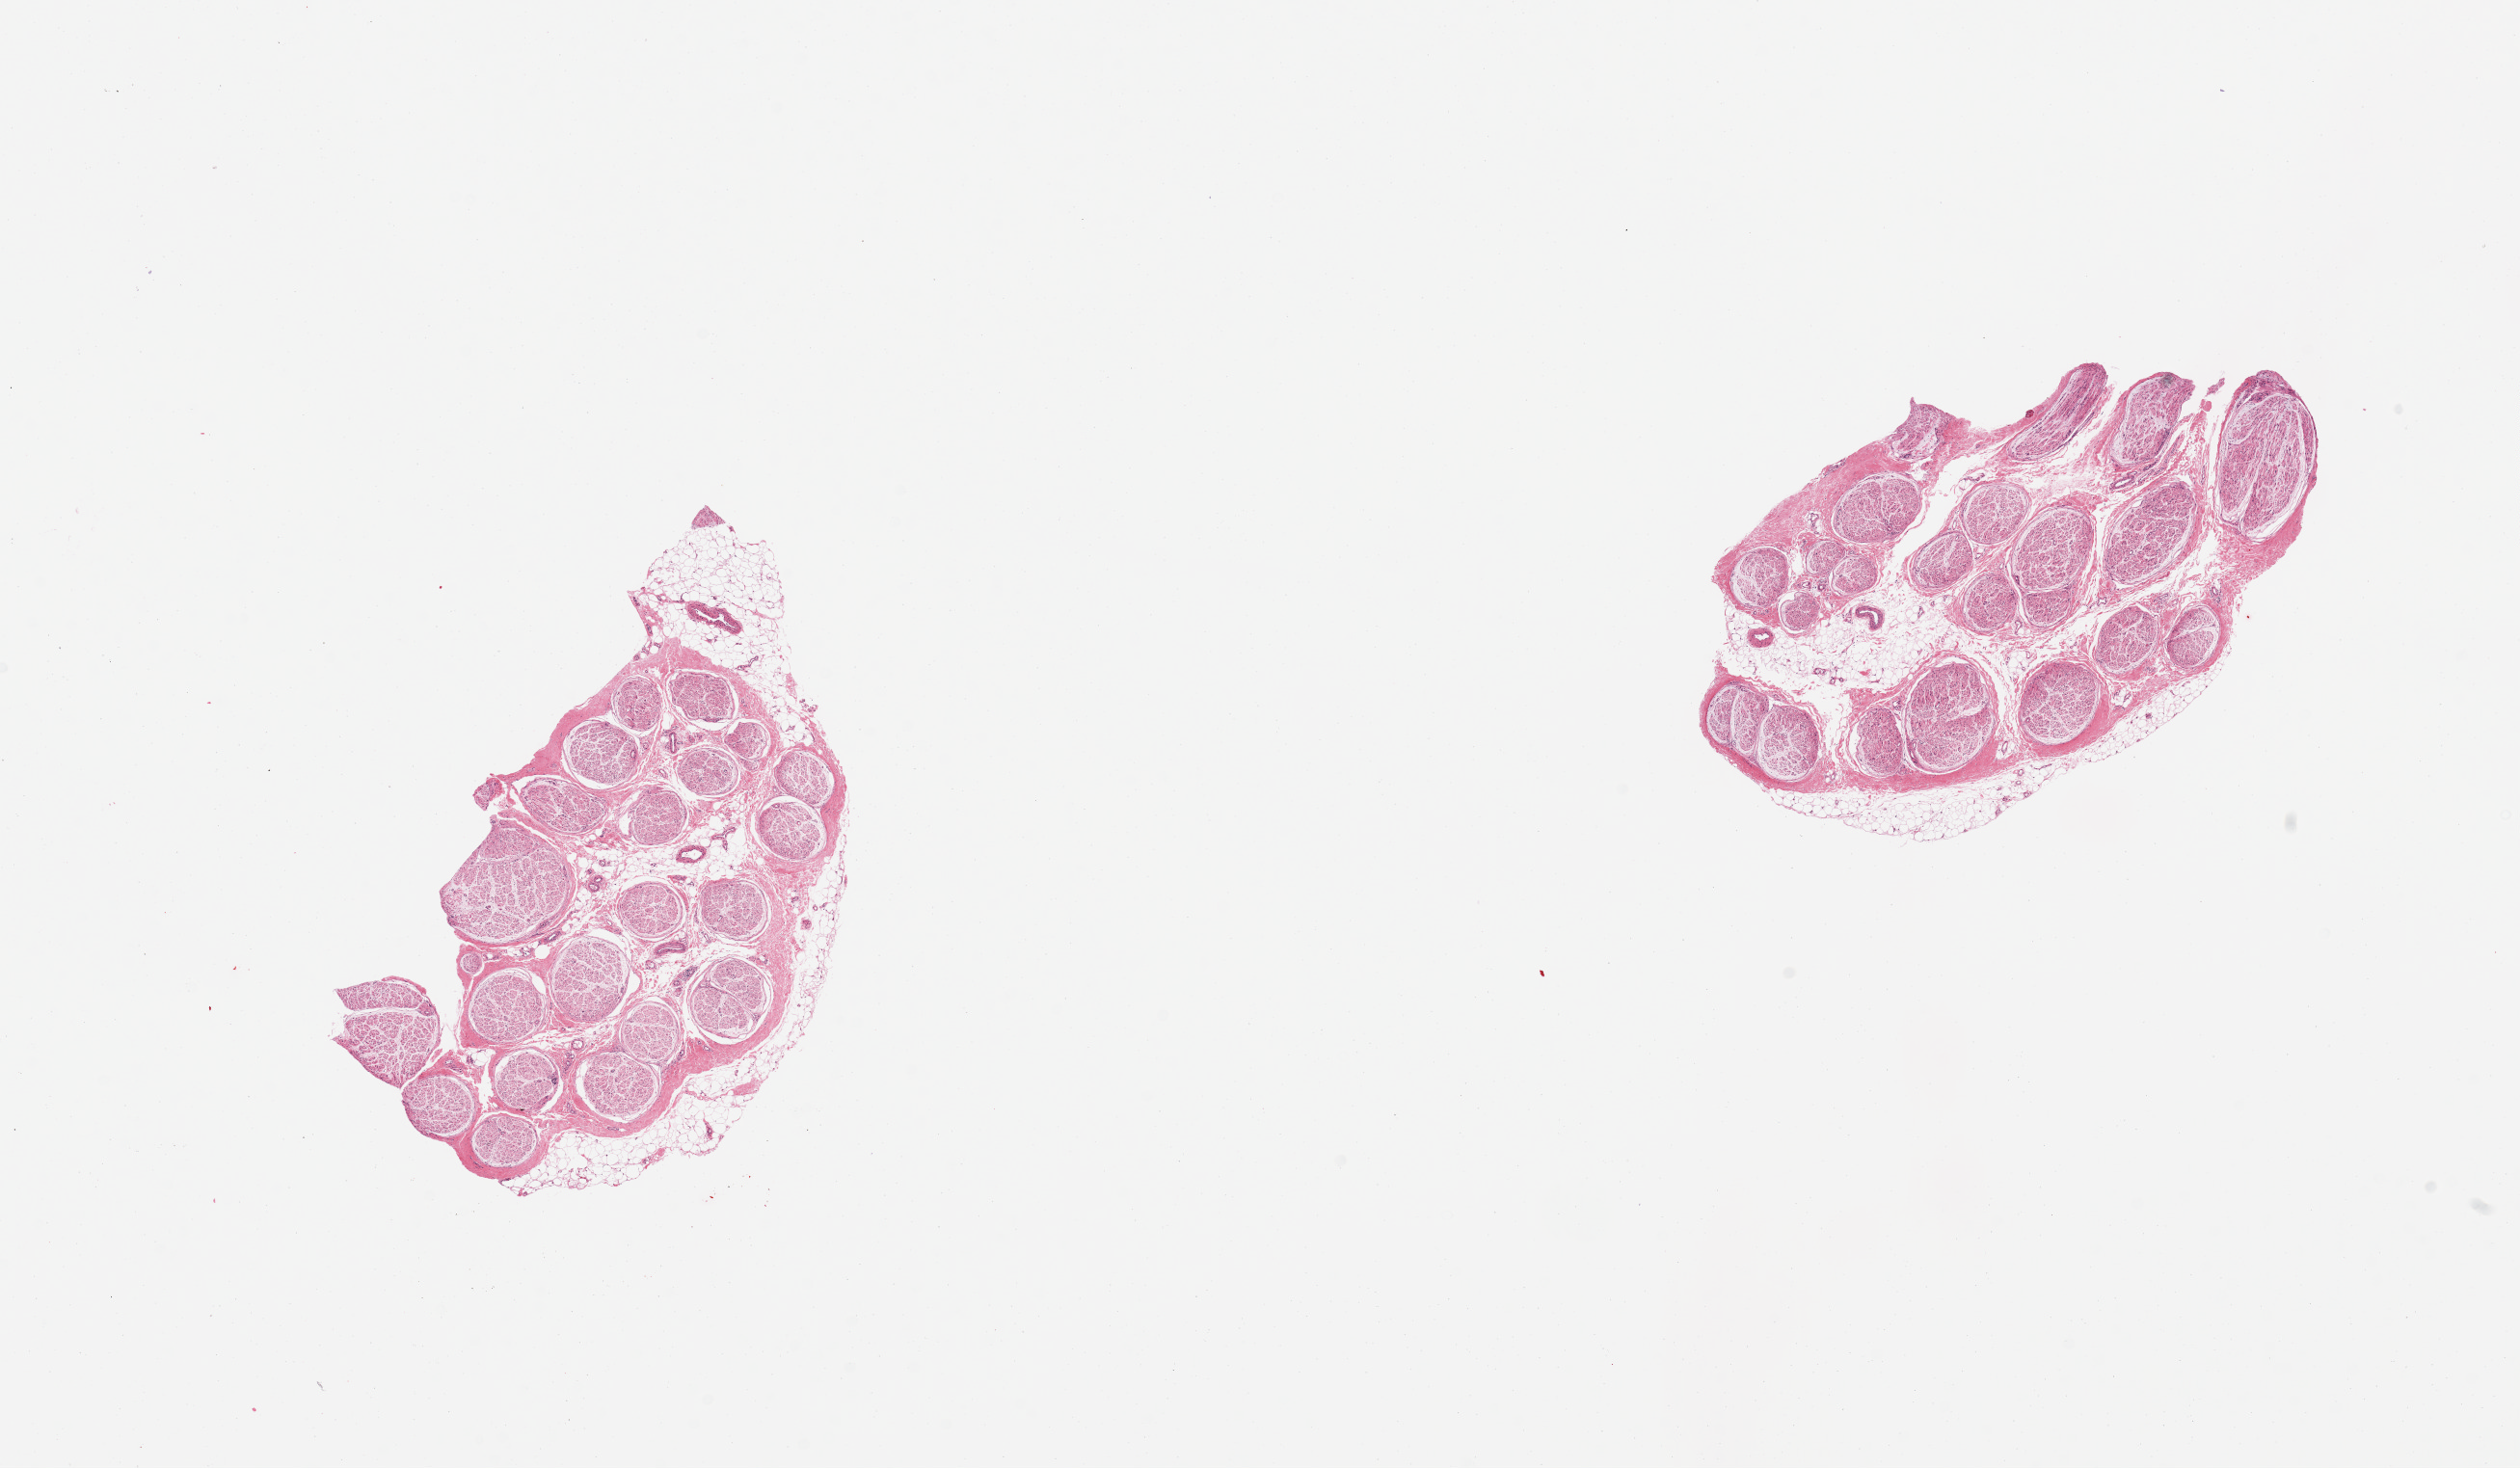
Haematoxylin and eosin whole-slide image, whole scanned area (about 20.7 x 12.0 mm) shown as a low-resolution overview, PAXgene-fixed paraffin-embedded (PFPE) section, target tissue: tibial nerve, donor tissue sample.
* reviewer comment on this tissue sample: 2 pieces; 10 & 30% internal fat; 10 & 30 % external fat